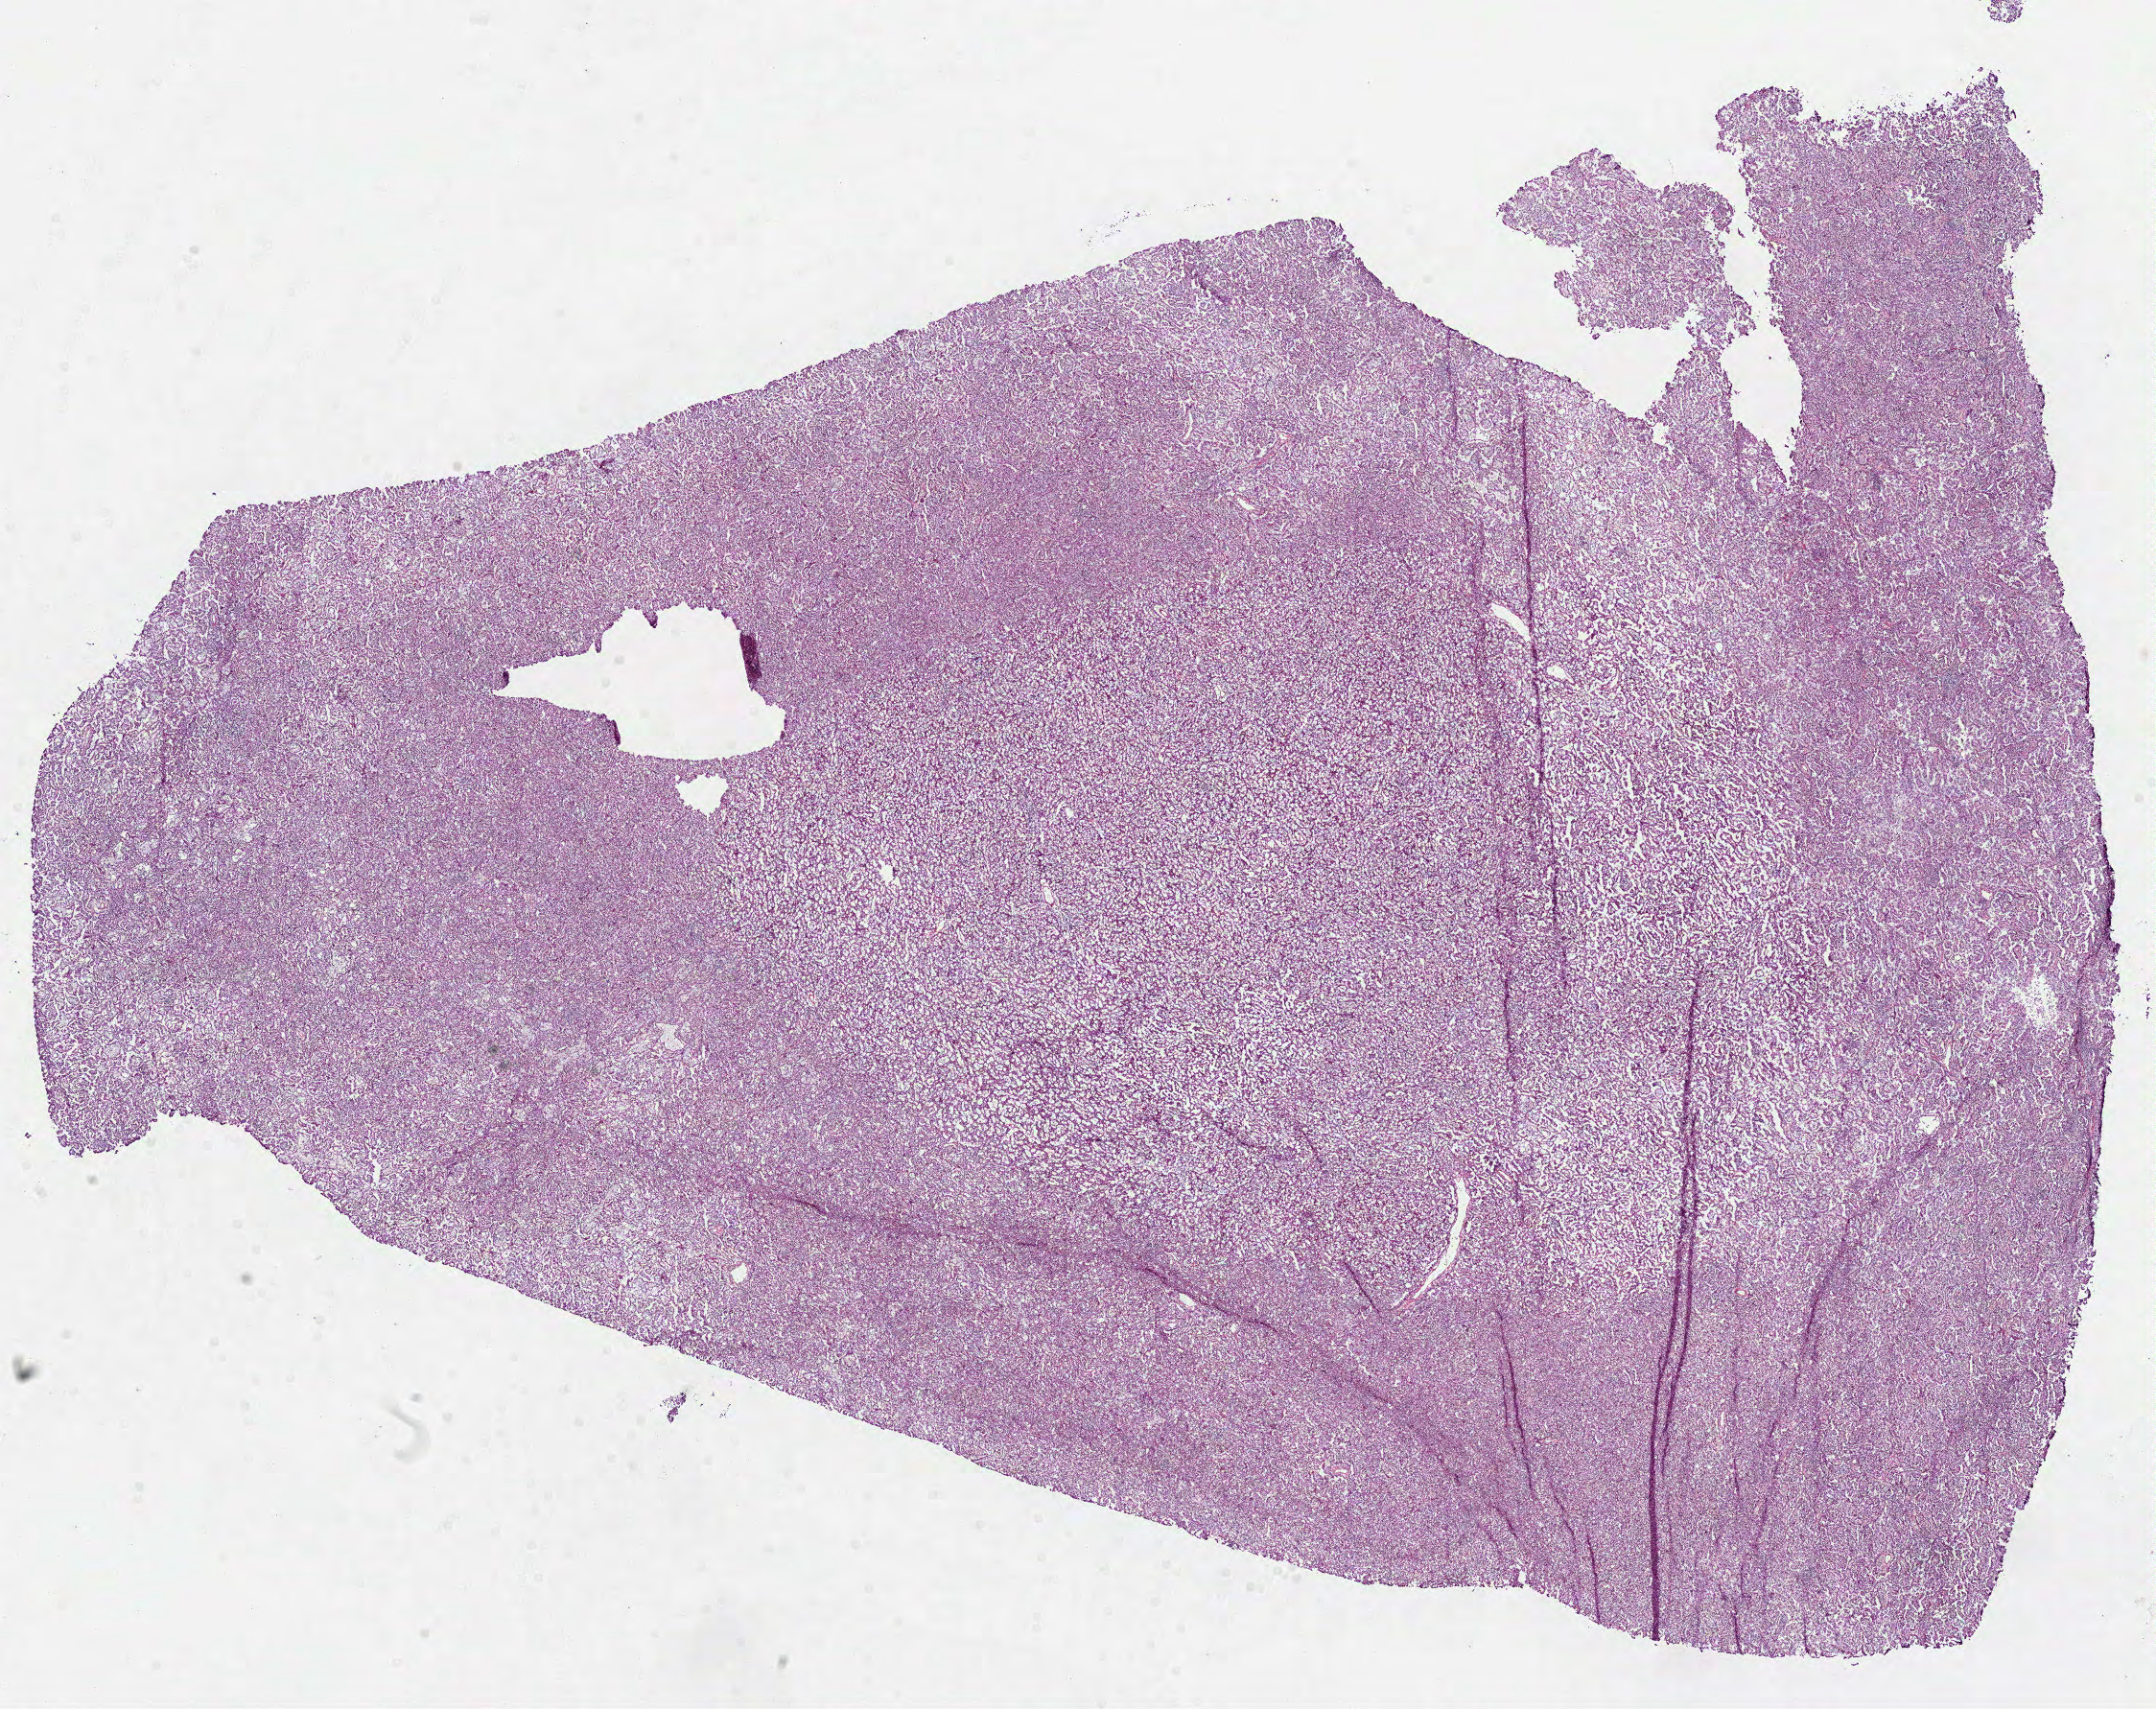
Digitized Hematoxylin and eosin (H&E) stained tissue section (whole slide) — shown as a low-resolution overview of the whole scanned area (about 18.1 x 14.4 mm), frozen section from the bottom of the tissue portion, kidney, primary tumour sample. Male patient; age at initial diagnosis 61 years. Pathologist review of this section (percent, as recorded): tumour cells 100%, tumour nuclei 85%, normal cells 0%, stromal cells 0%, necrosis 0%. Infiltration values recorded for this section: lymphocyte infiltration 3%, monocyte infiltration 2%, neutrophil infiltration 2%.
Histologic diagnosis: Papillary adenocarcinoma, NOS. AJCC pathologic stage: I (7th edition).